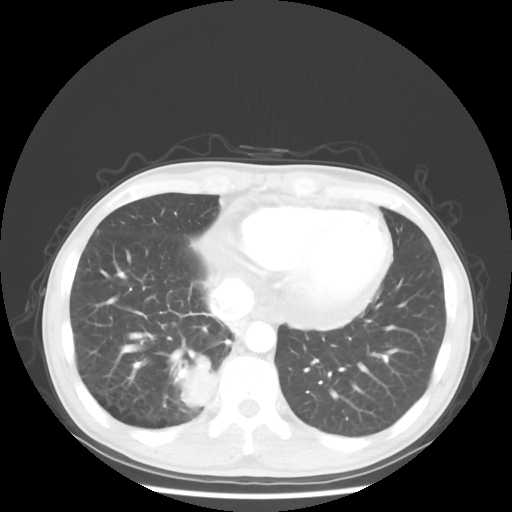
Chest CT, one axial slice. Slice 13 of 58 in the series (ordered by position). Reconstruction kernel STANDARD. 100 kVp. Lung window (W 1500 / L -600 HU). 5 mm slice thickness. 512 × 512 image matrix, field of view 360 × 360 mm. Male patient, age 56 years. From the clinical record (not read from this slice): clinical TNM (as recorded): T2 N1 M1; histopathological grade: G1.
Outlined on this slice (bounding box drawn by a radiologist):
- lung tumour (recorded histology: adenocarcinoma): bounding box (x1, y1, x2, y2) in pixels: (175, 353, 220, 414)